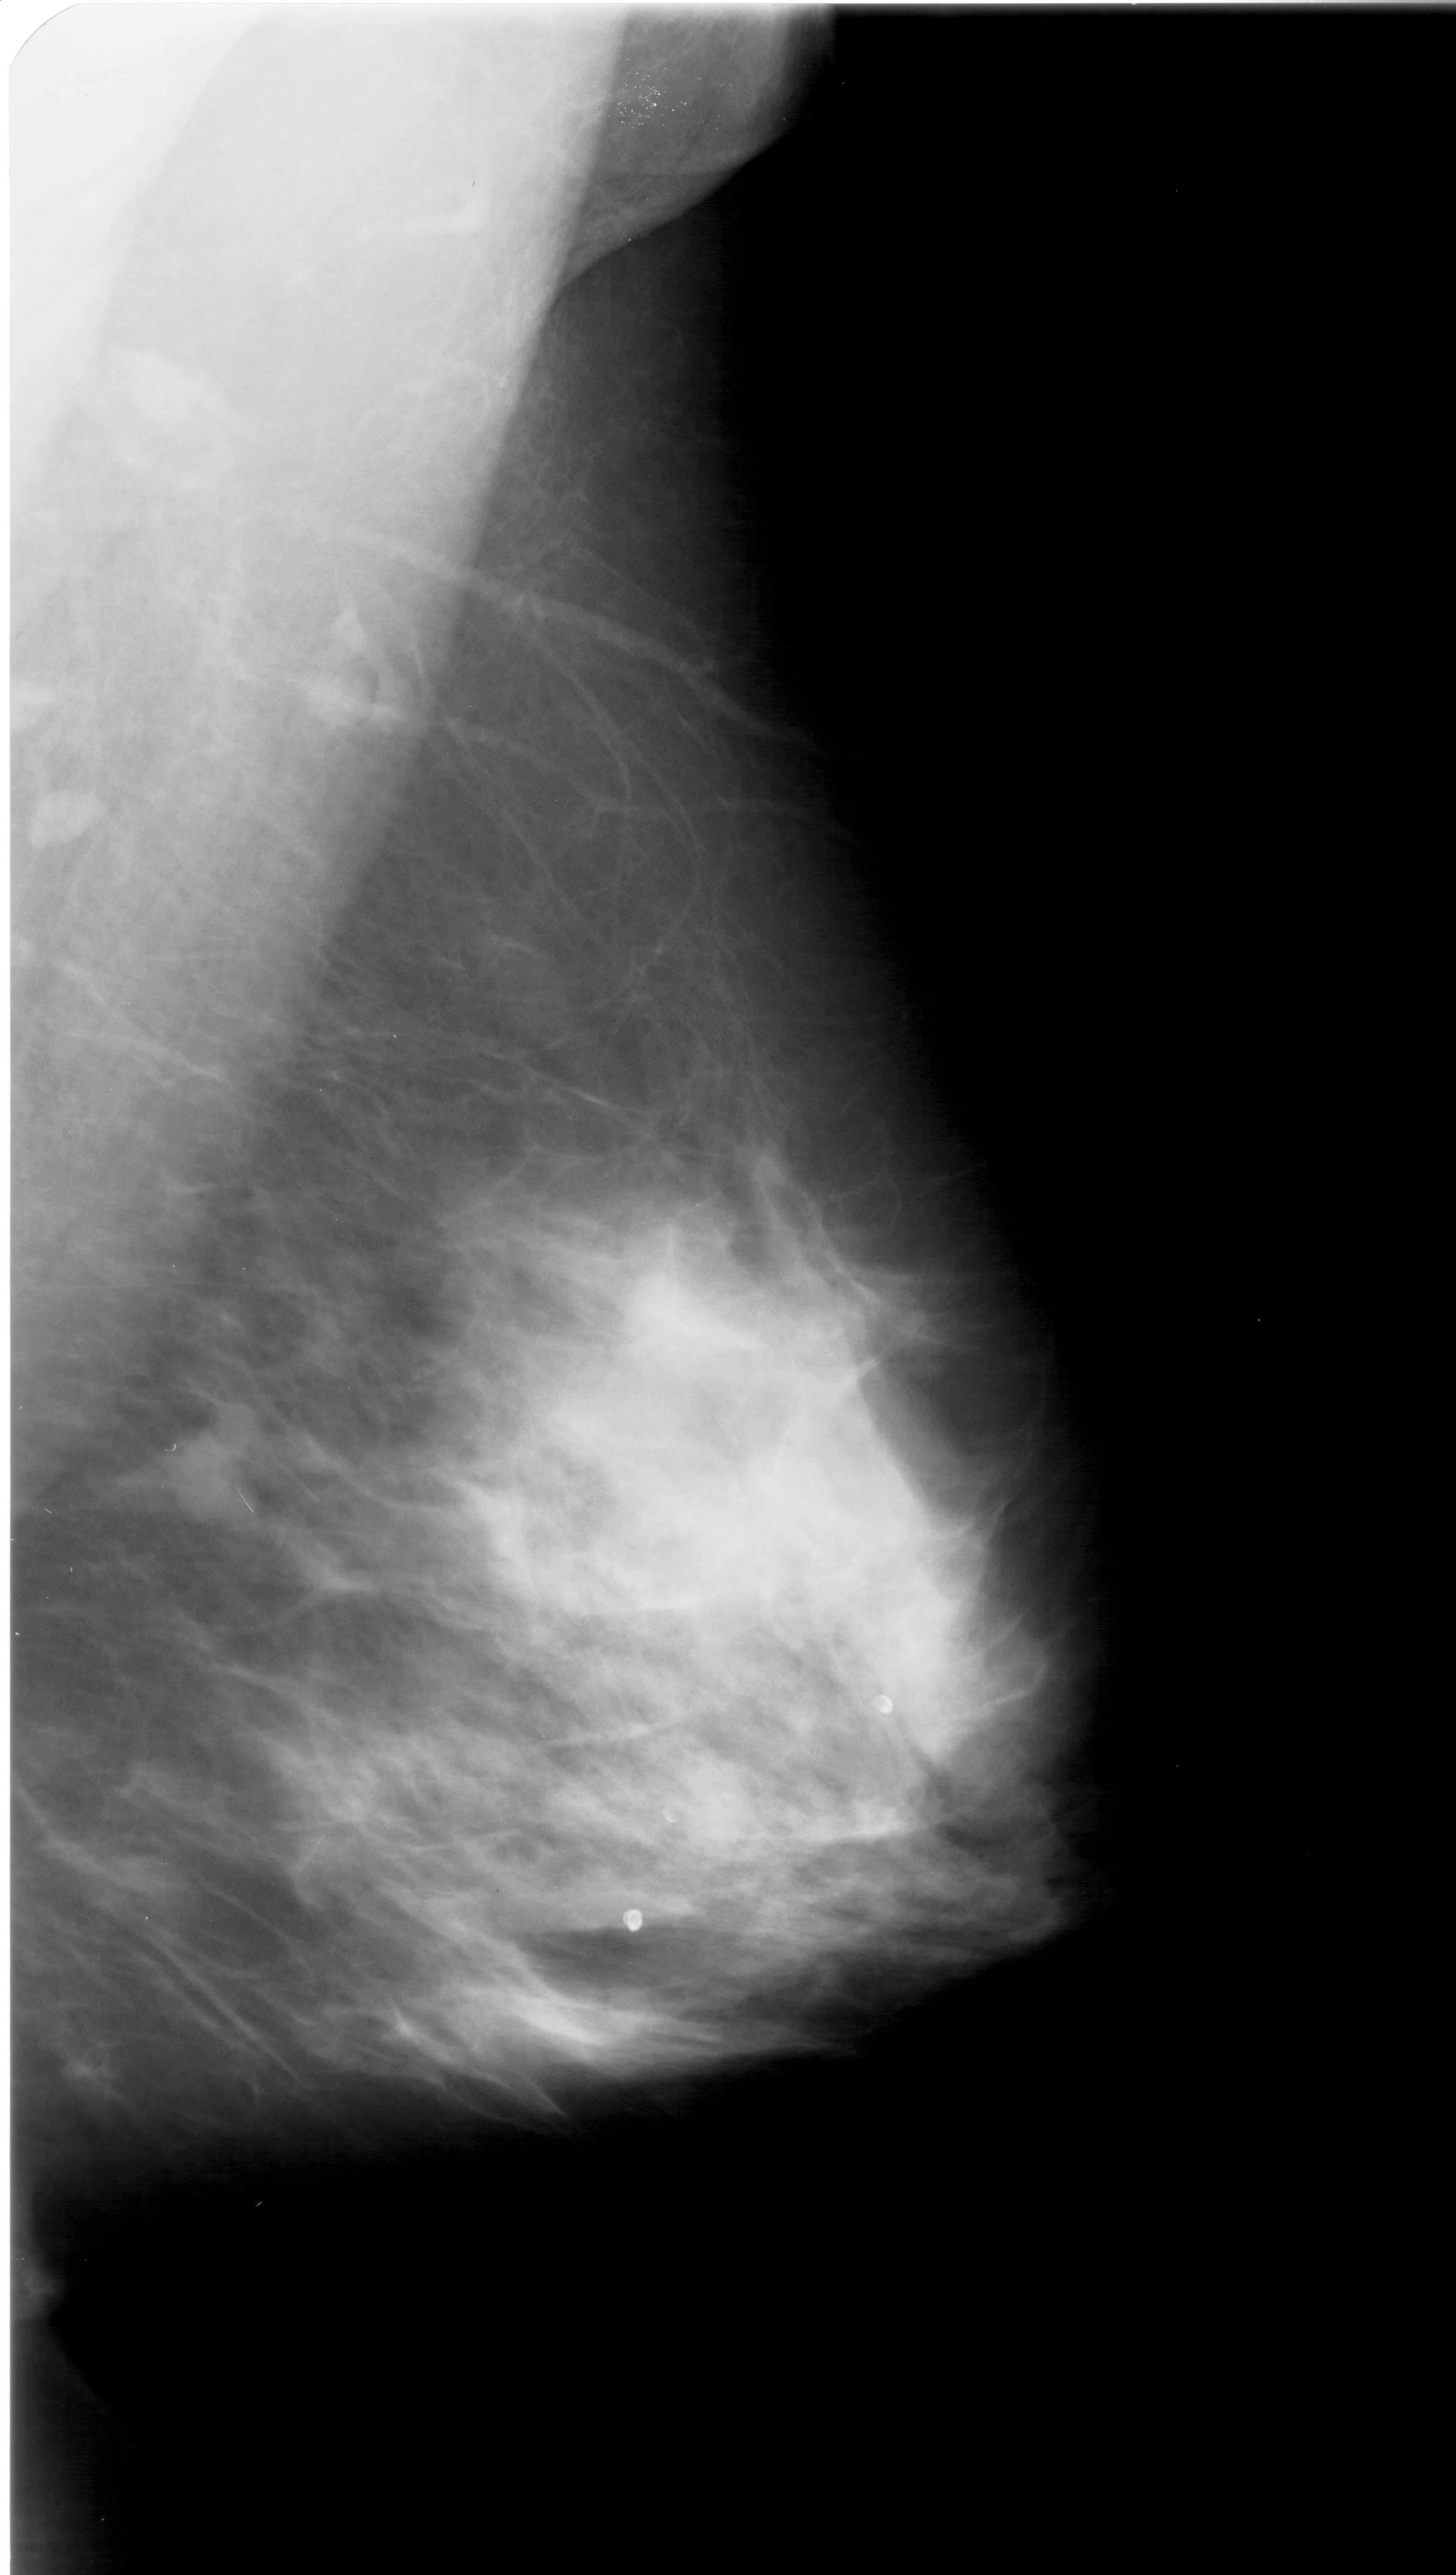
Mammogram (digitized film); right breast; MLO view; breast composition: extremely dense (BI-RADS density category 4 of 4); 1456 × 2575 image matrix.
Marked abnormalities (boxes around the expert regions of interest):
- mass, shape lobulated, margins ill defined; BI-RADS assessment category 4; subtlety rating 2 on a 1 (subtle) to 5 (obvious) scale; pathology result (as recorded, not read from the image): malignant: bounding box (x1, y1, x2, y2) in pixels: (167, 1428, 246, 1517)